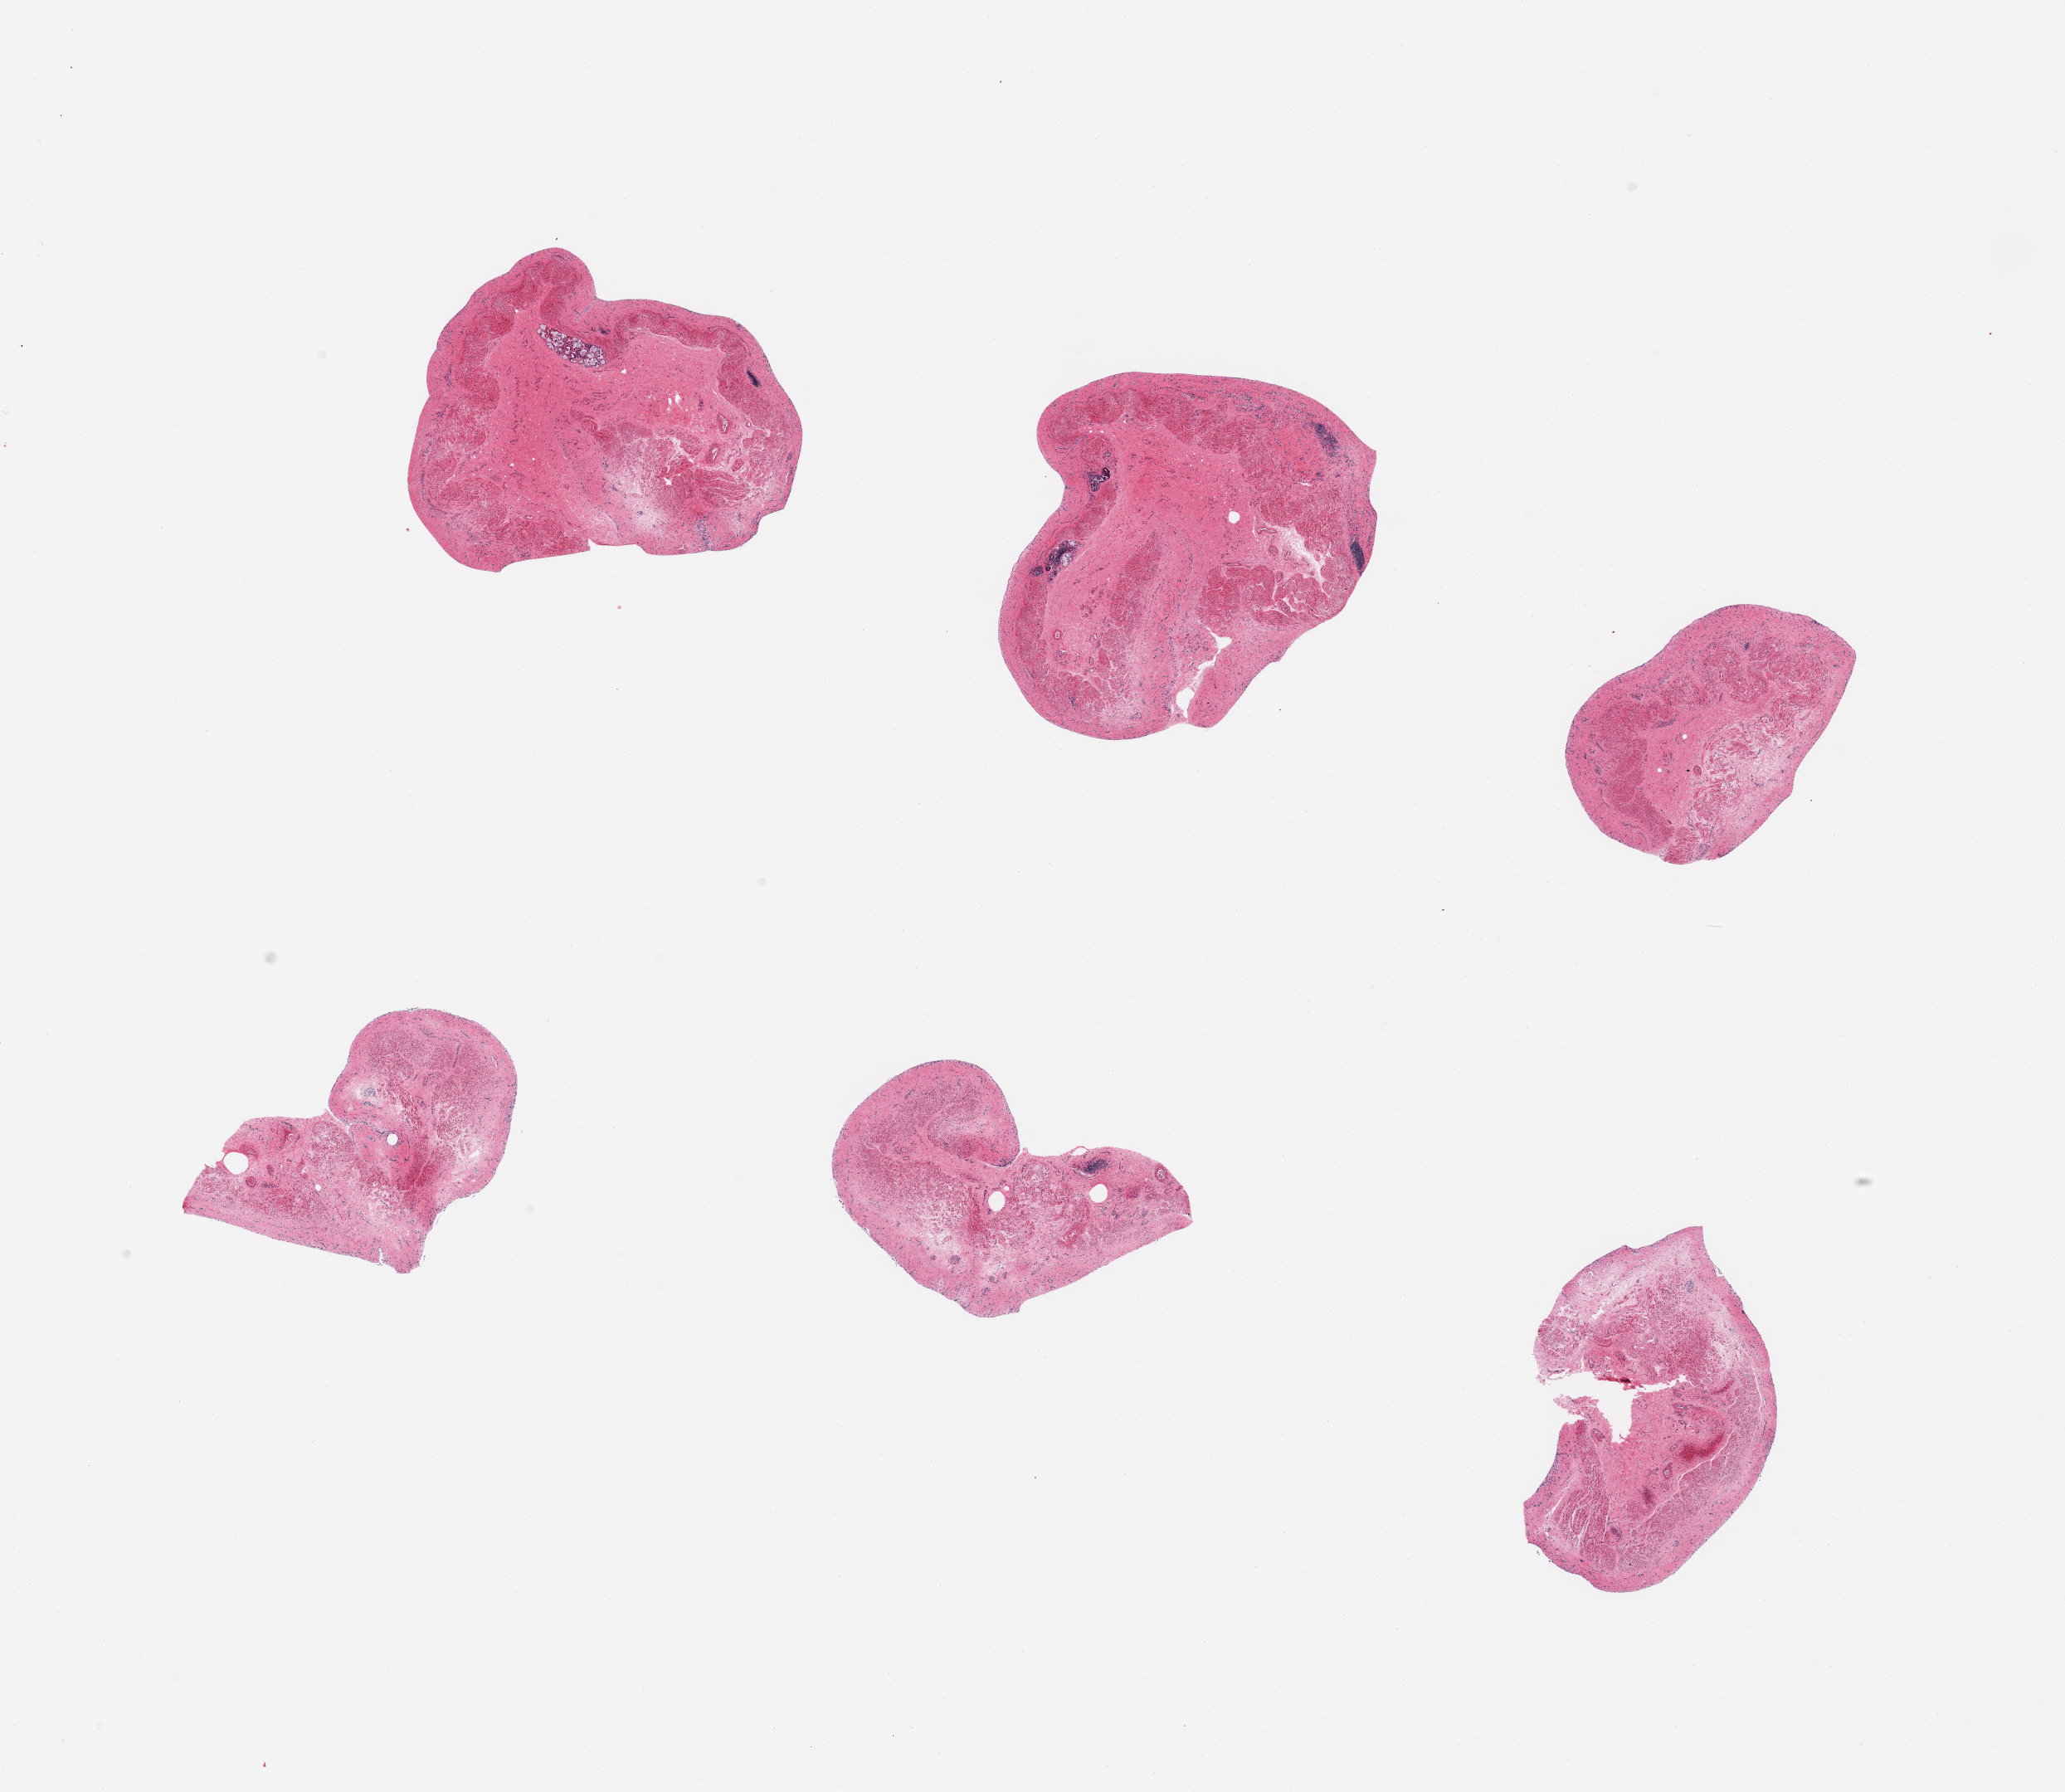
Whole-slide image, haematoxylin and eosin stain, brightfield — whole scanned area (about 19.7 x 17.1 mm, from a 20x scan) shown as a low-resolution overview, PAXgene-fixed paraffin-embedded (PFPE) section, section of esophageal mucous membrane (target tissue), tissue donor sample.
Review note (as recorded): 6 pieces, no target mucosa; completely sloughed.